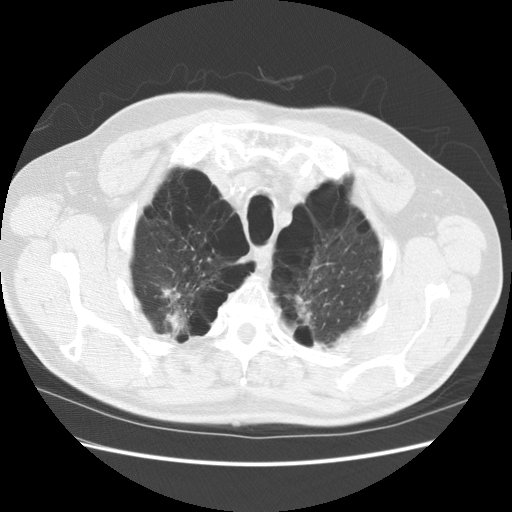
Axial slice from a low-dose chest CT screening exam; first (baseline) screen; lung window (W 1500 / L -600 HU); 512 × 512 image matrix, field of view 360 × 360 mm. Male, age 68 years at enrolment. Former smoker at enrolment.
• Expert reader's lesion annotation, bounding box (x1, y1, x2, y2) in pixels: (116, 273, 220, 341).
• The screening reader recorded 2 non-calcified nodules or masses ≥4 mm on this exam (left lower lobe, lingula); which of them this box marks is not recorded.
• Official screen result: positive, change unspecified: nodule(s) >= 4 mm or enlarging nodule(s), mass(es), or other non-specific abnormalities suspicious for lung cancer.